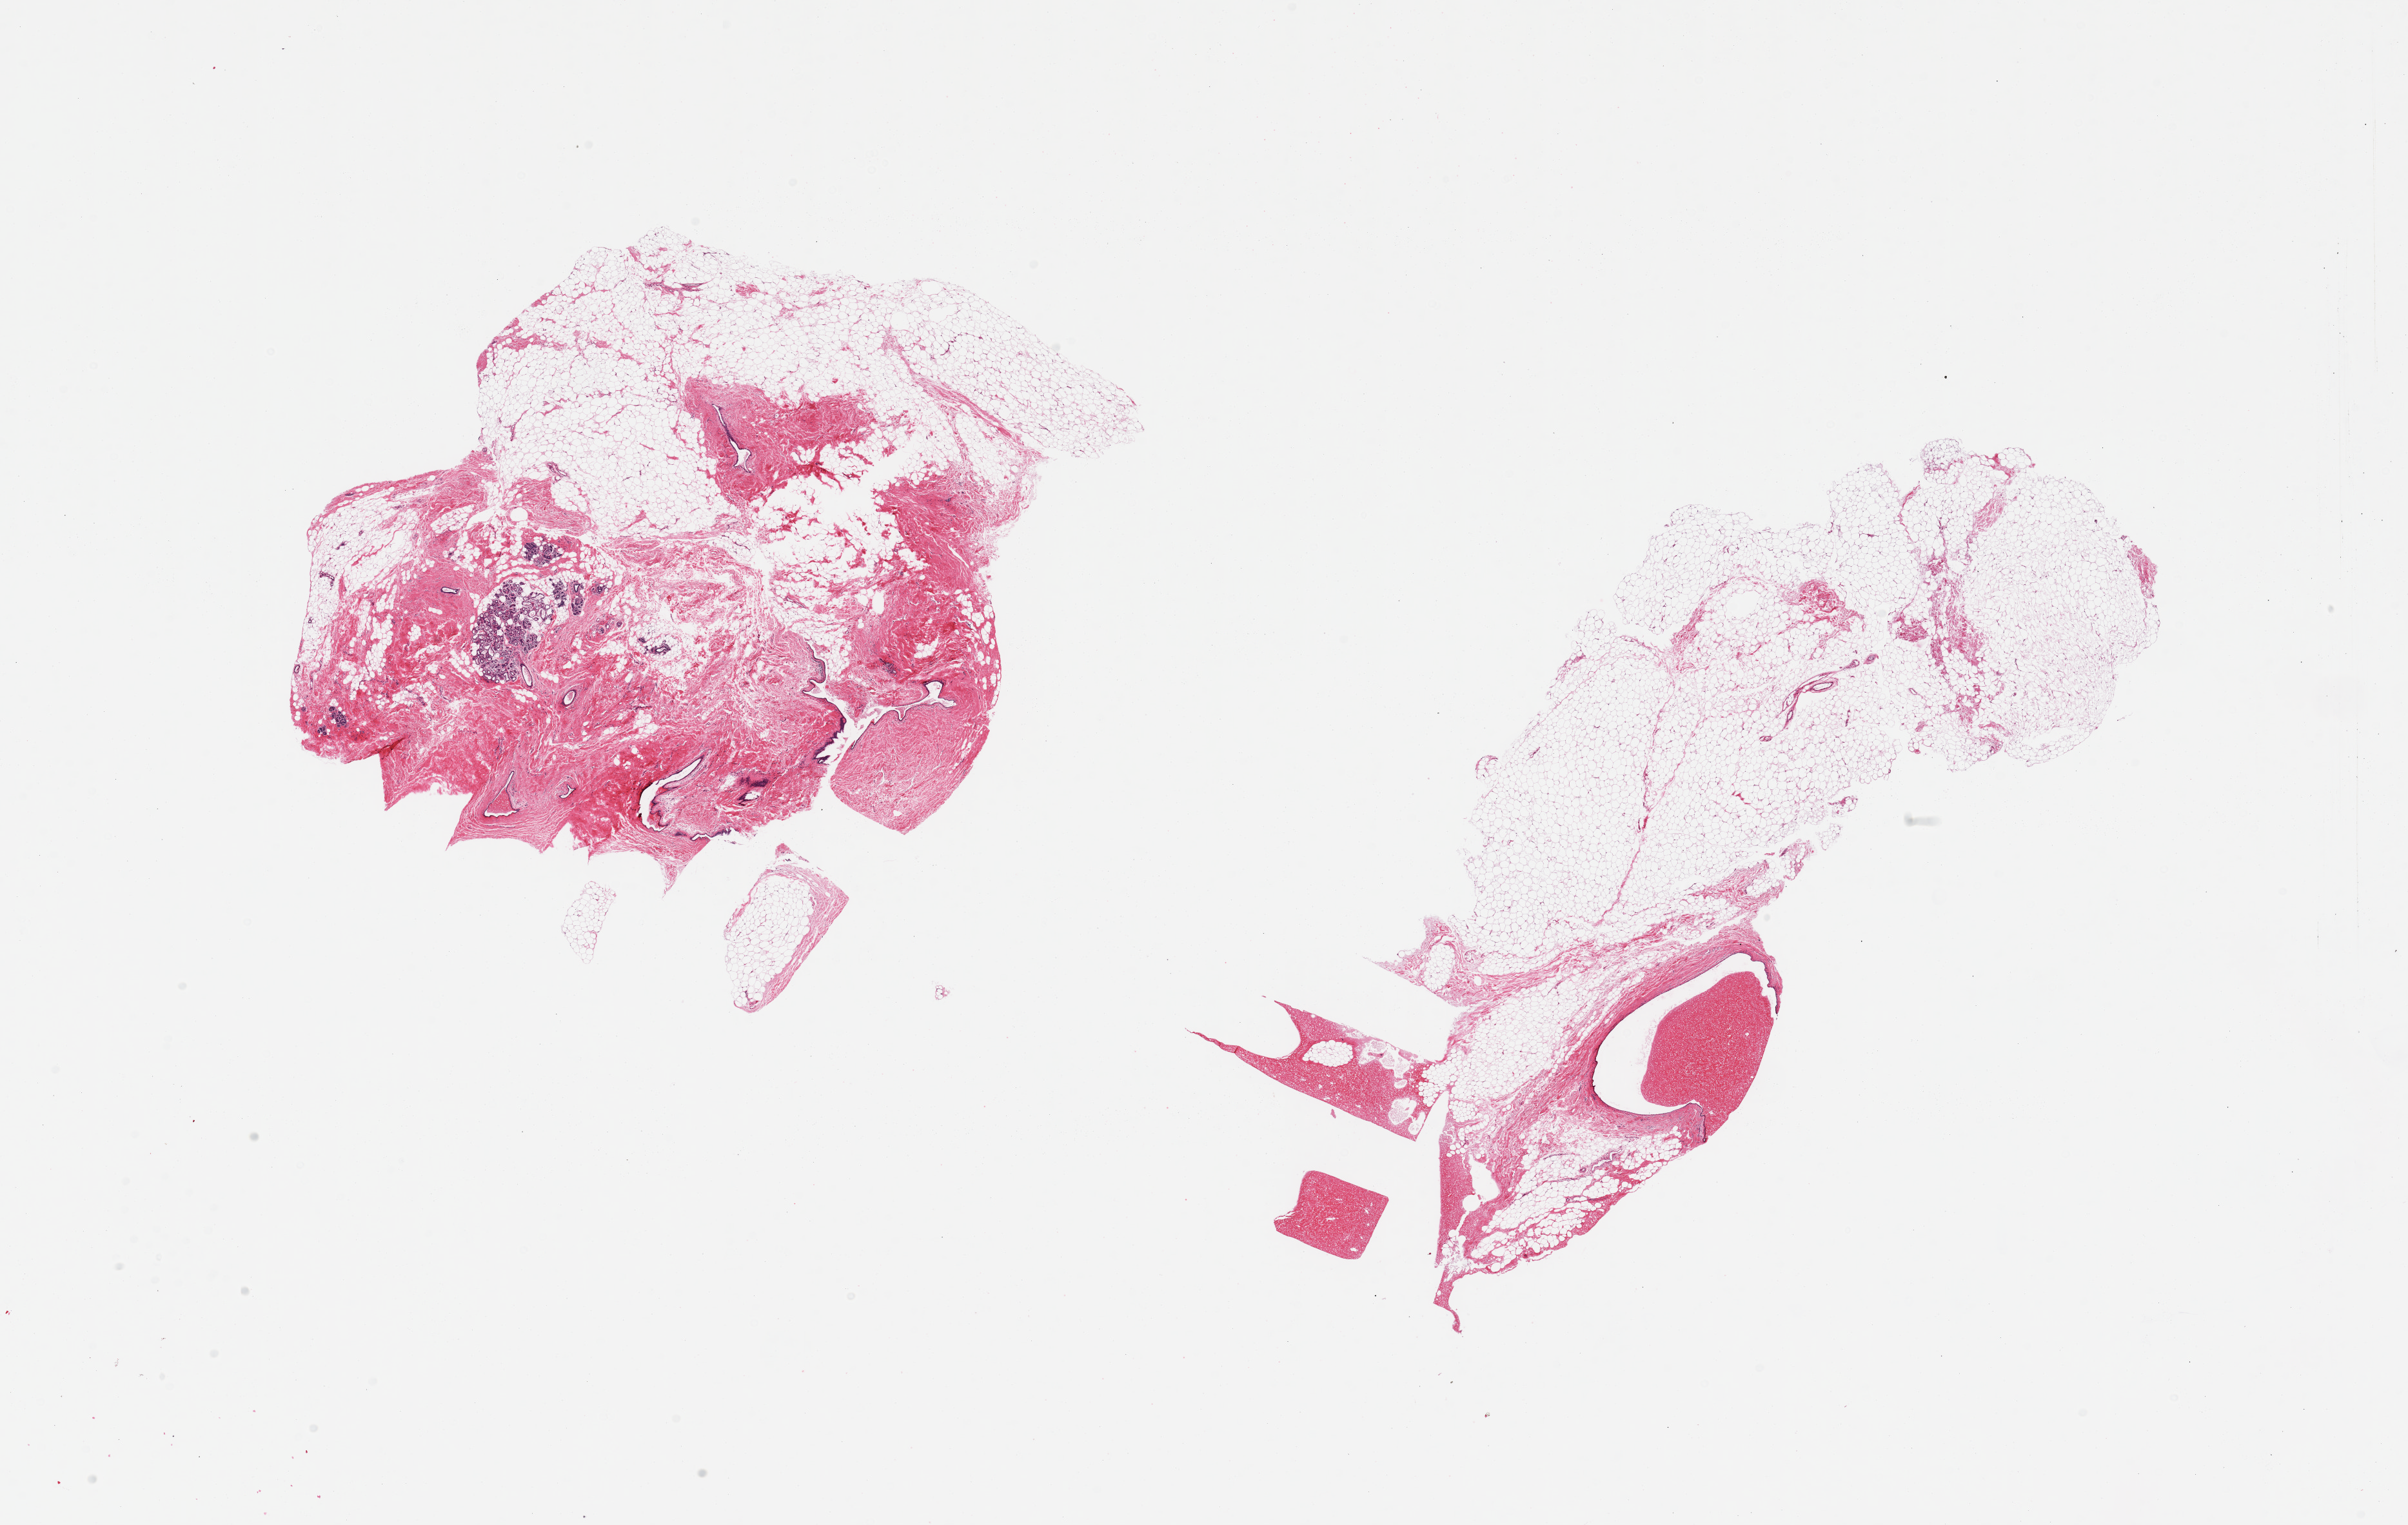
Hematoxylin and eosin (H&E) whole-slide image, shown as a low-resolution overview of the whole scanned area (about 29.5 x 18.7 mm, slide scanned at 20x). PAXgene-fixed paraffin-embedded (PFPE) section. Sampled site (target tissue): breast. Tissue donor sample. Donor: female.
Review note (as recorded): 2 pieces, mainly fibradipose elements; focal duct/lobular elements.